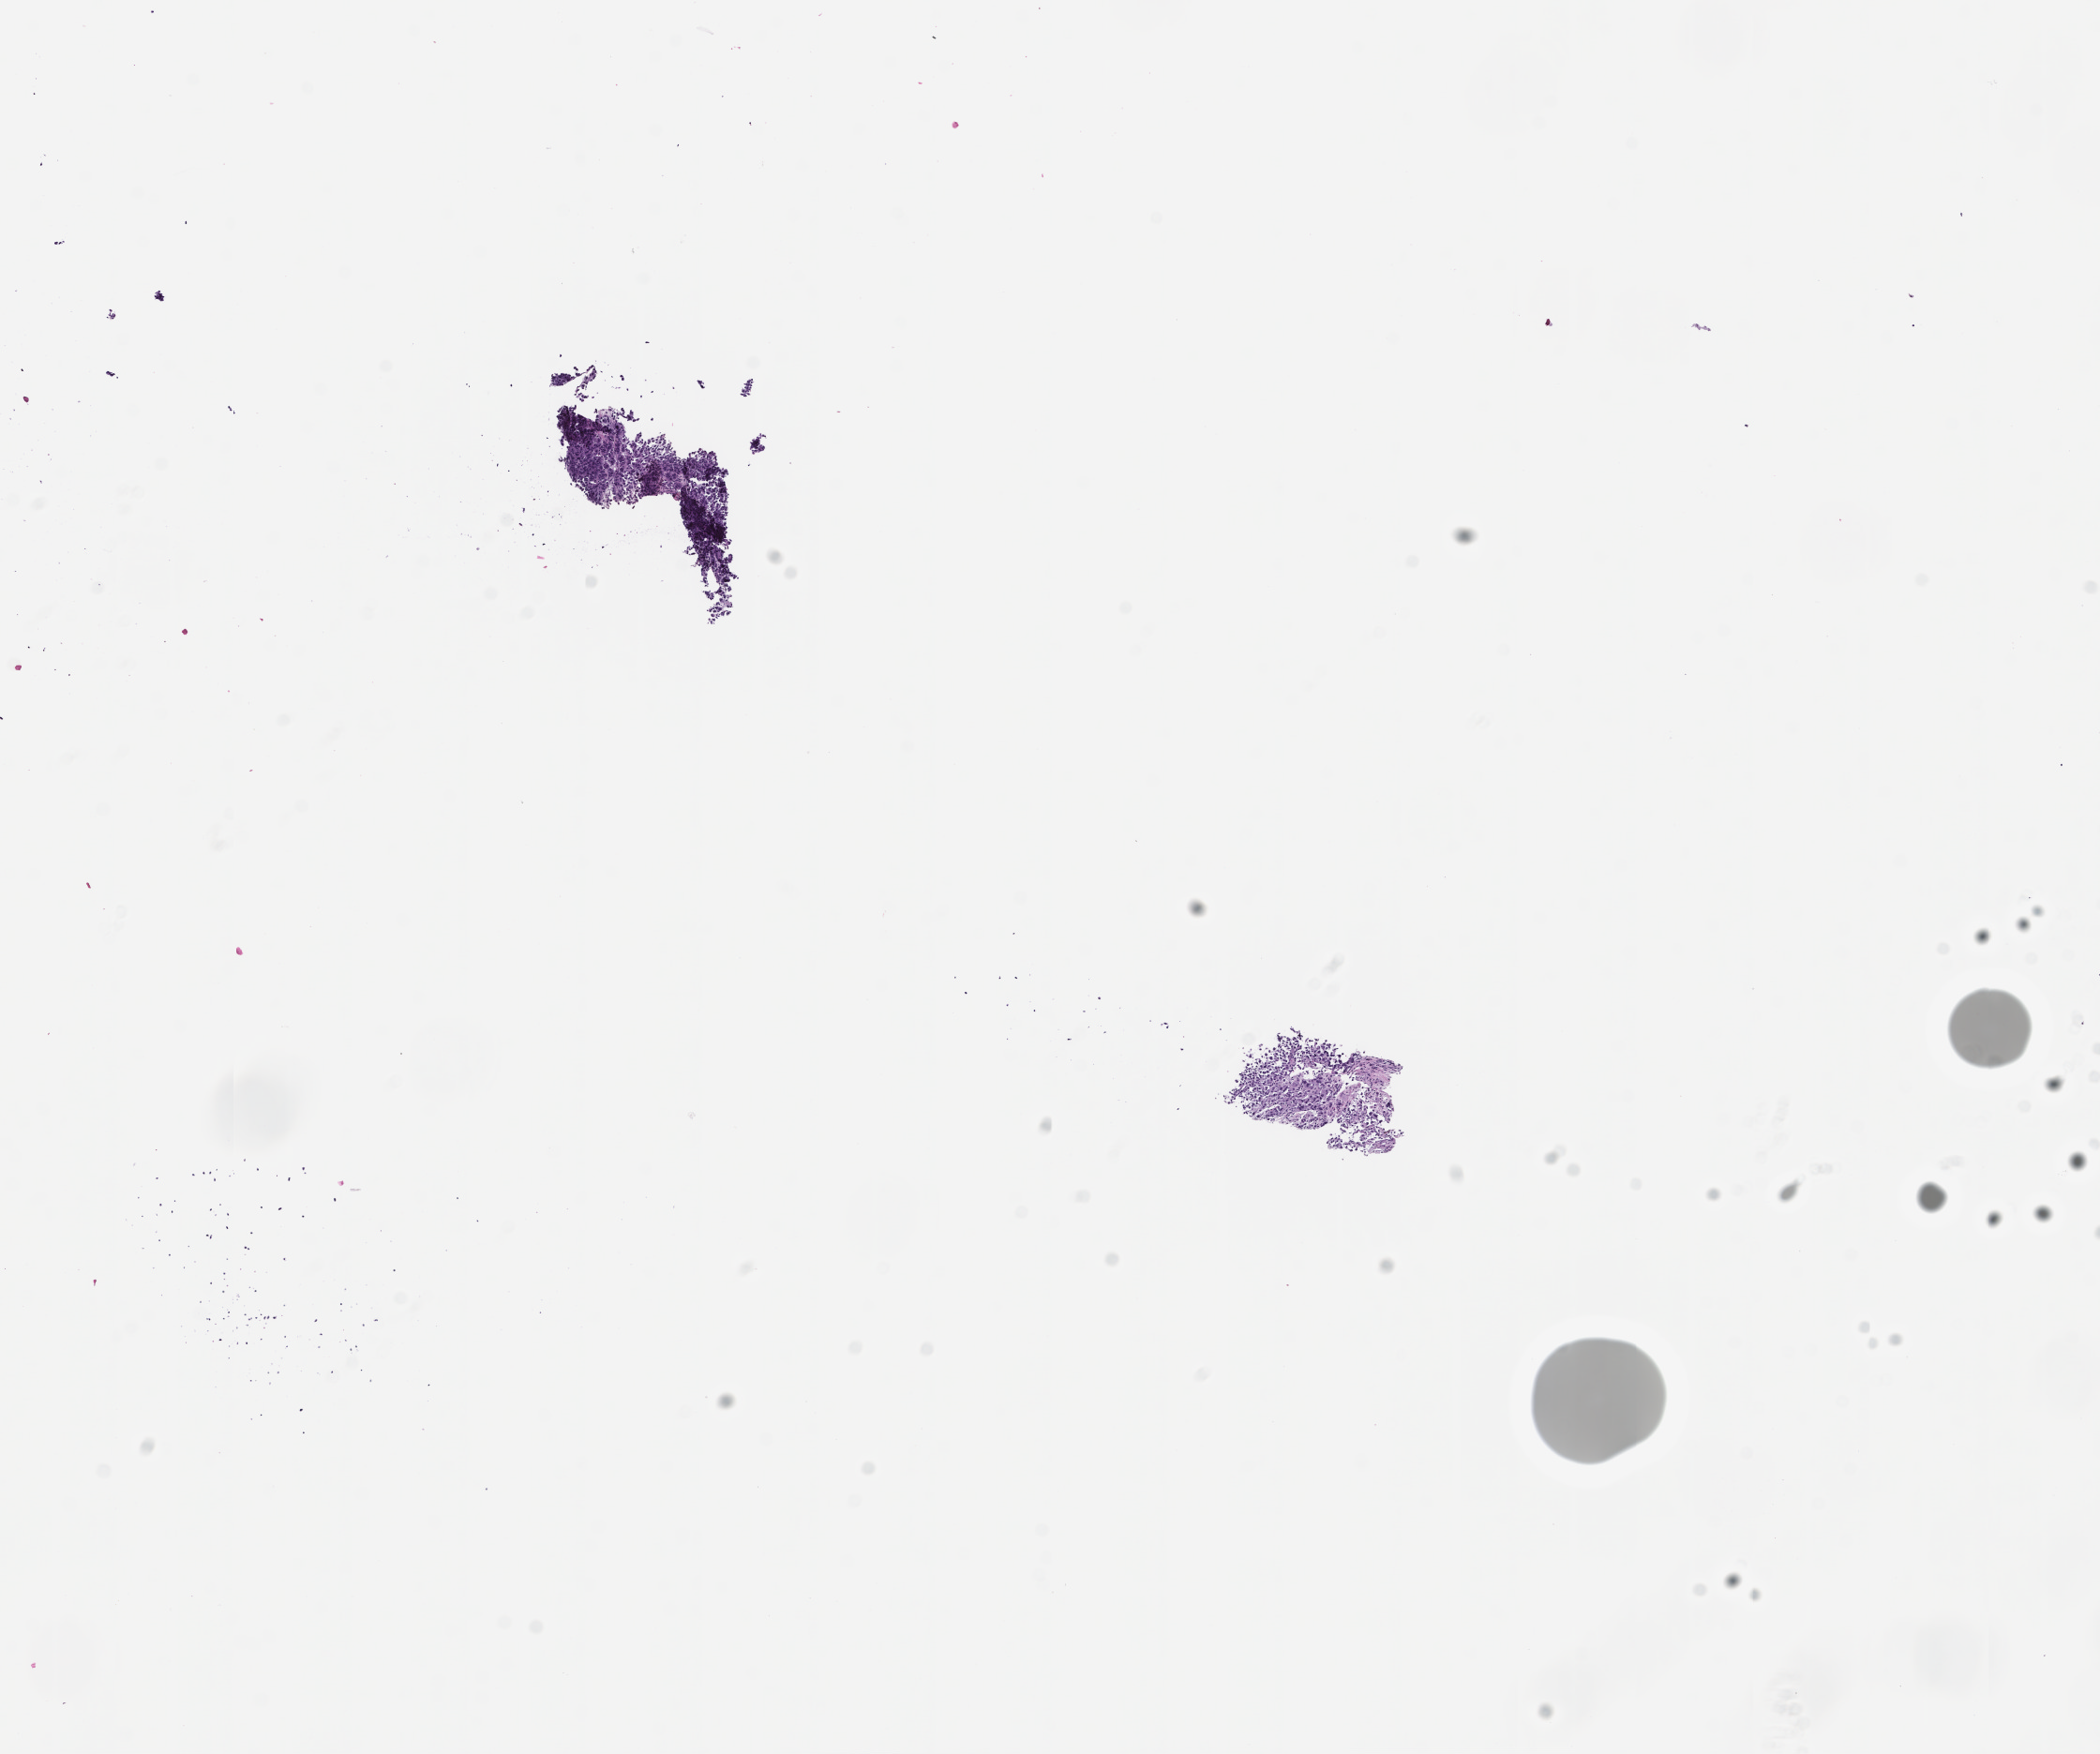
Whole-slide image, hematoxylin and eosin (H&E) stain — a low-resolution overview of the entire scanned area, about 9.0 x 7.6 mm. Formalin-fixed paraffin-embedded section. Collected at baseline (before treatment). Male patient.
This section: metastatic tumor tissue. Patient diagnosis (primary): Melanoma.